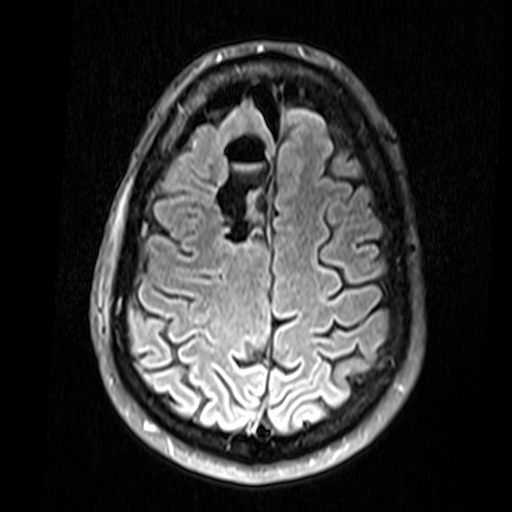
Brain MRI from a brain-tumour surgery series, one axial slice; slice 49 of 74 in the series (ordered by position); T2 FLAIR; 3.3 mm slice thickness; 512 × 512 image matrix, field of view 220 × 220 mm. From the clinical record (not read from this slice): histopathology: Glial fibroma; tumour location: Right Frontal.
Annotated regions visible in this slice (expert manual segmentation):
- residual tumour: bounding box <219,191,263,256> (left, top, right, bottom; pixels)